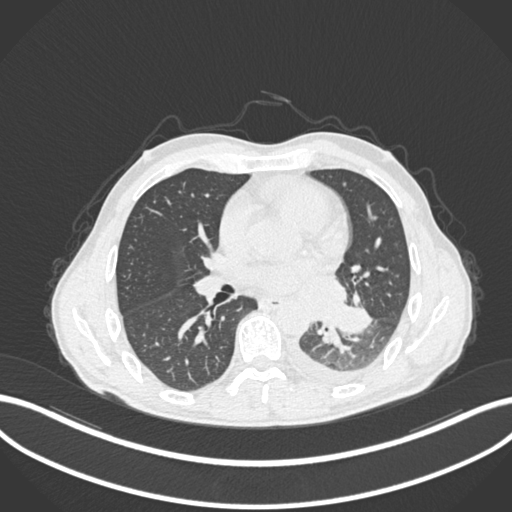
Chest CT, one axial slice; position 120 of 222 along the scan axis; 120 kVp; lung window (W 1500 / L -600 HU); 1 mm slice thickness; 512 × 512 image matrix. Male patient, age 47 years. Case-level facts recorded for this patient, not image findings: clinical TNM (as recorded): T3 N1 M1c.
Outlined on this slice (bounding box drawn by a radiologist):
- lung tumour (recorded histology: small cell carcinoma): bounding box [x1, y1, x2, y2] px = [328, 301, 374, 337]